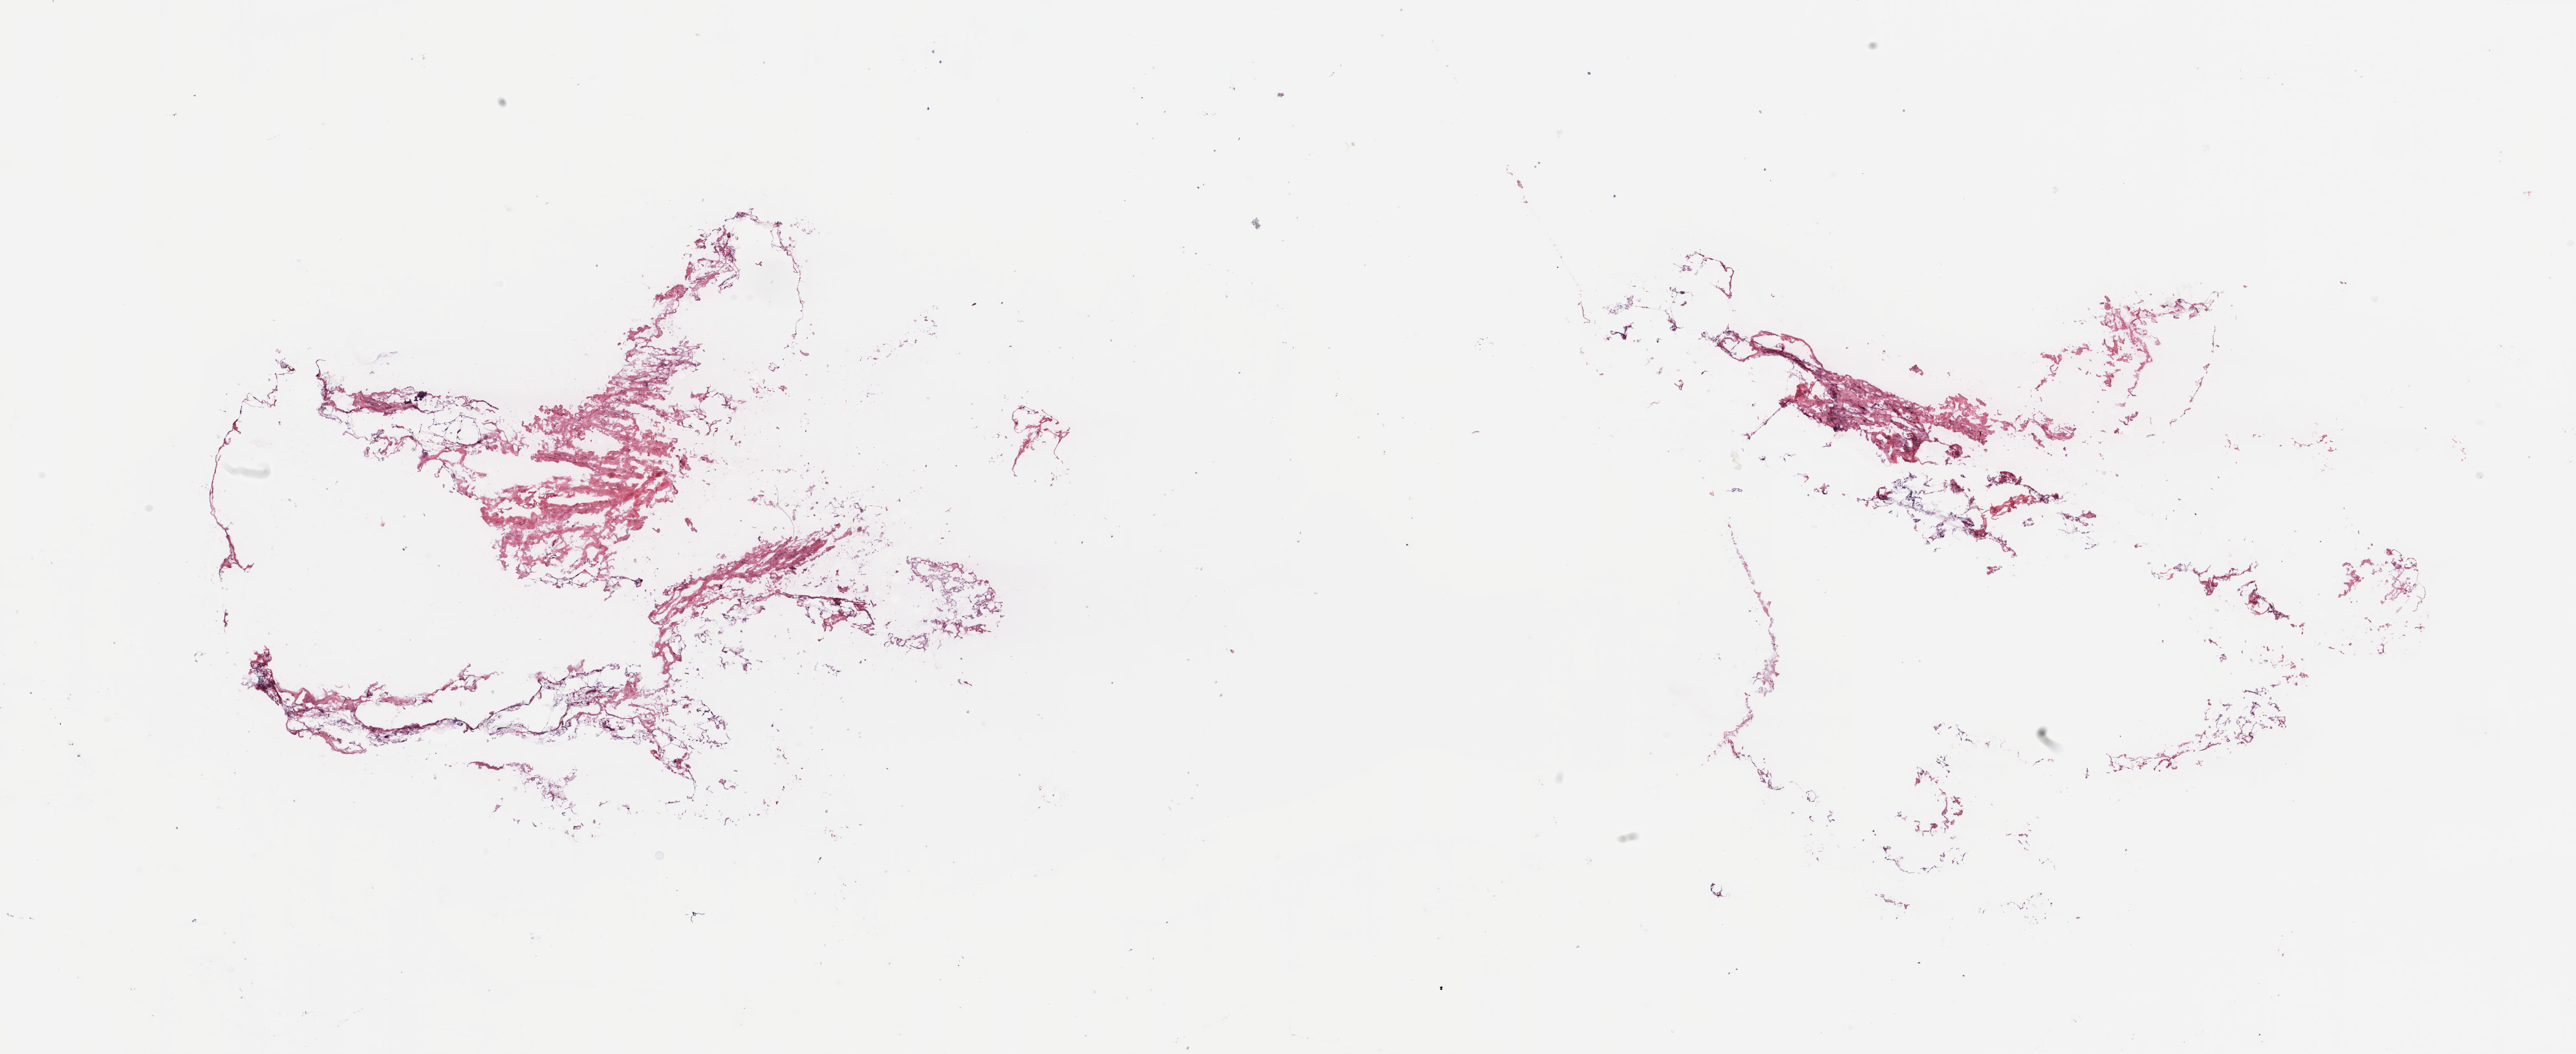
Digitized H&E tissue section (whole slide), a low-resolution overview of the entire scanned area, about 31.5 x 12.9 mm; breast, tissue type not recorded.
Patient diagnosis (cohort enrolment): breast cancer (breast).